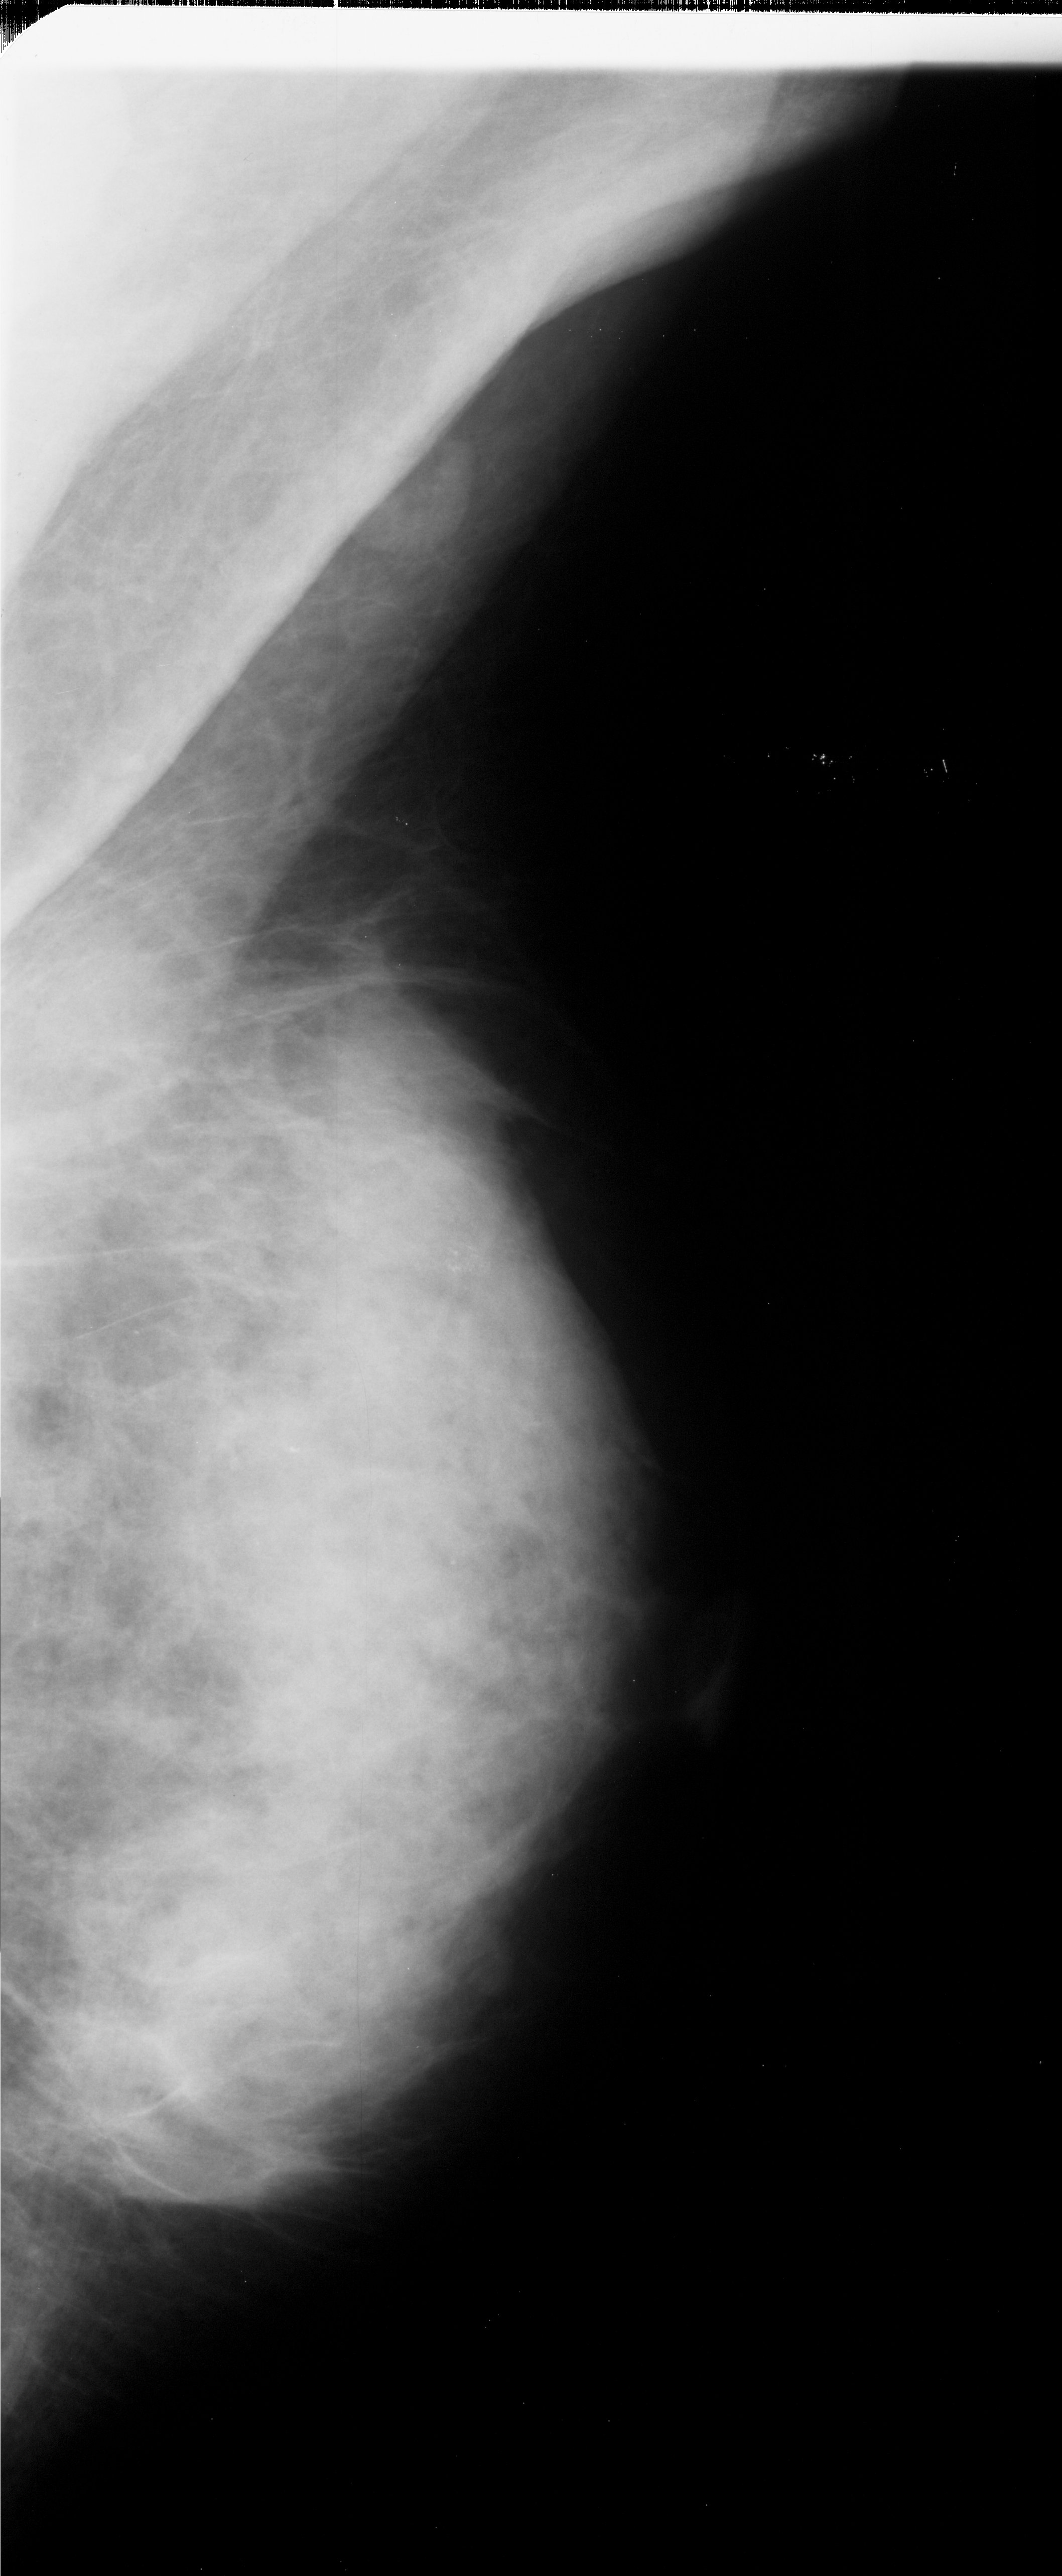
Mammogram (digitized film); right breast; mediolateral oblique (MLO) view; BI-RADS breast density category 4 (scale 1–4); 1062 × 2576 image matrix.
Marked abnormalities (boxes around the expert regions of interest):
- calcifications, morphology pleomorphic, distribution clustered; BI-RADS assessment category 4; subtlety rating 2 on a 1 (subtle) to 5 (obvious) scale; pathology (as recorded): malignant: box from (x=410, y=1218) to (x=501, y=1295) px